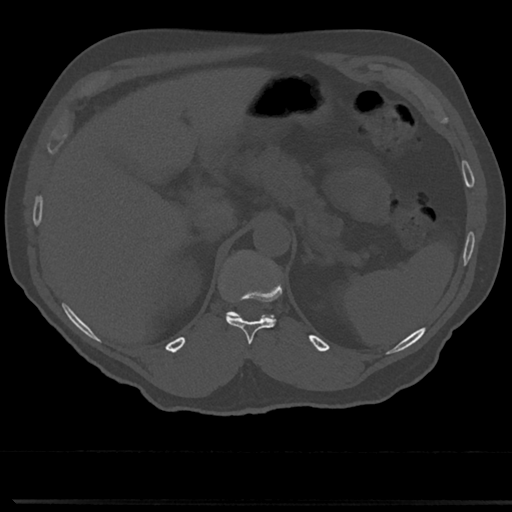
CT including the spine, one axial slice. Bone window (W 1800 / L 400 HU). 512 × 512 image matrix, field of view 355 × 355 mm. Male patient, age 61 years. Case-level facts recorded for this patient, not image findings: primary cancer: prostate.
Annotated regions visible in this slice (semi-automatic segmentation, software-assisted and operator-edited):
- T11 vertebra: bounding box (x1, y1, x2, y2) in pixels: (226, 293, 277, 346)
- T12 vertebra: (224, 250, 276, 320)